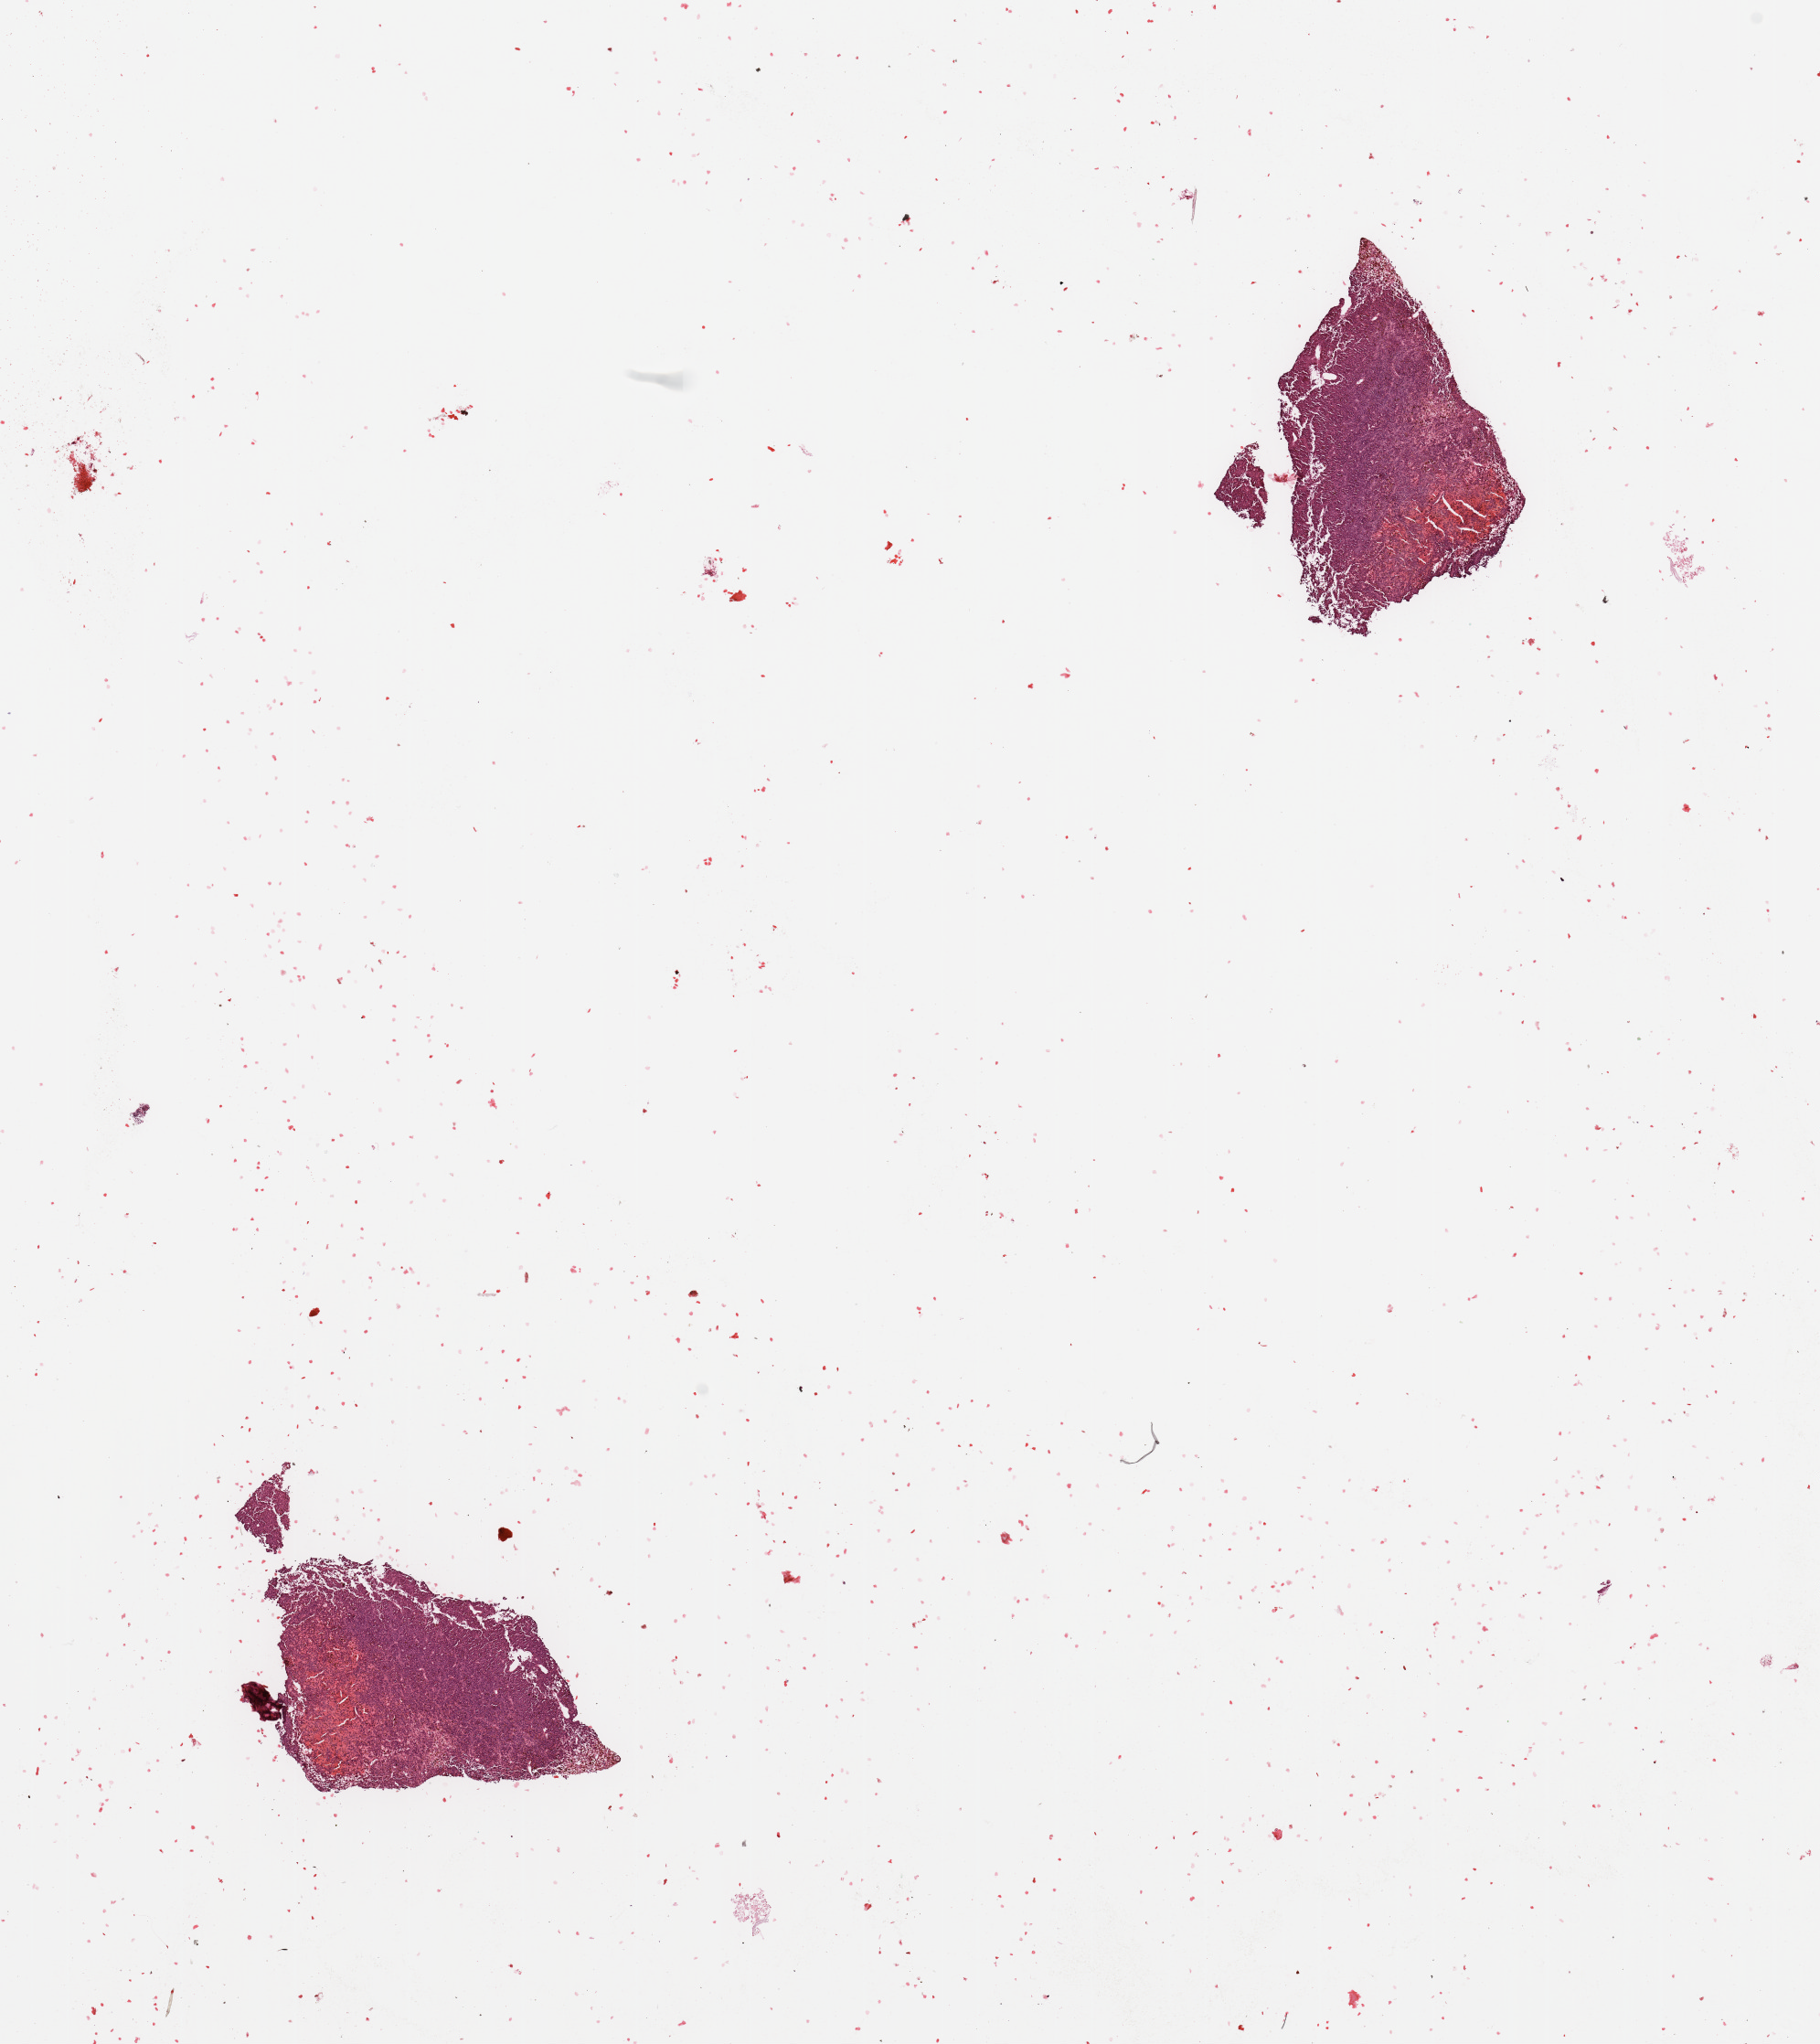
Whole-slide histology image, H&E — a low-resolution overview of the entire scanned area, about 15.8 x 17.7 mm, tumour tissue sample, sampled site: lymph node. Male, 76 y/o. Pathologist review of this section (percent, as recorded): tumour nuclei 90%, necrosis 5%.
• this section: metastatic tumour tissue
• patient diagnosis: Malignant melanoma, NOS